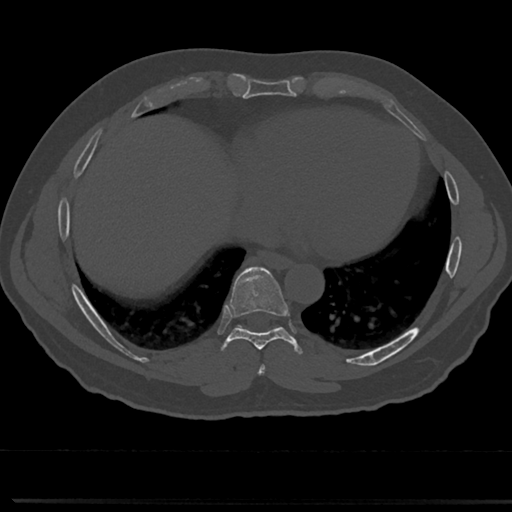
CT including the spine, one axial slice; reconstruction kernel Br40s/3; bone window (W 1800 / L 400 HU); 0.5 mm slice thickness; 512 × 512 image matrix. Patient: male, 61 years. Case-level facts recorded for this patient, not image findings: primary cancer: prostate.
Annotated regions visible in this slice (semi-automatic segmentation, software-assisted and operator-edited):
- T7 vertebra: box from (x=255, y=340) to (x=269, y=376) px
- T8 vertebra: (x=218, y=271)–(x=302, y=352)